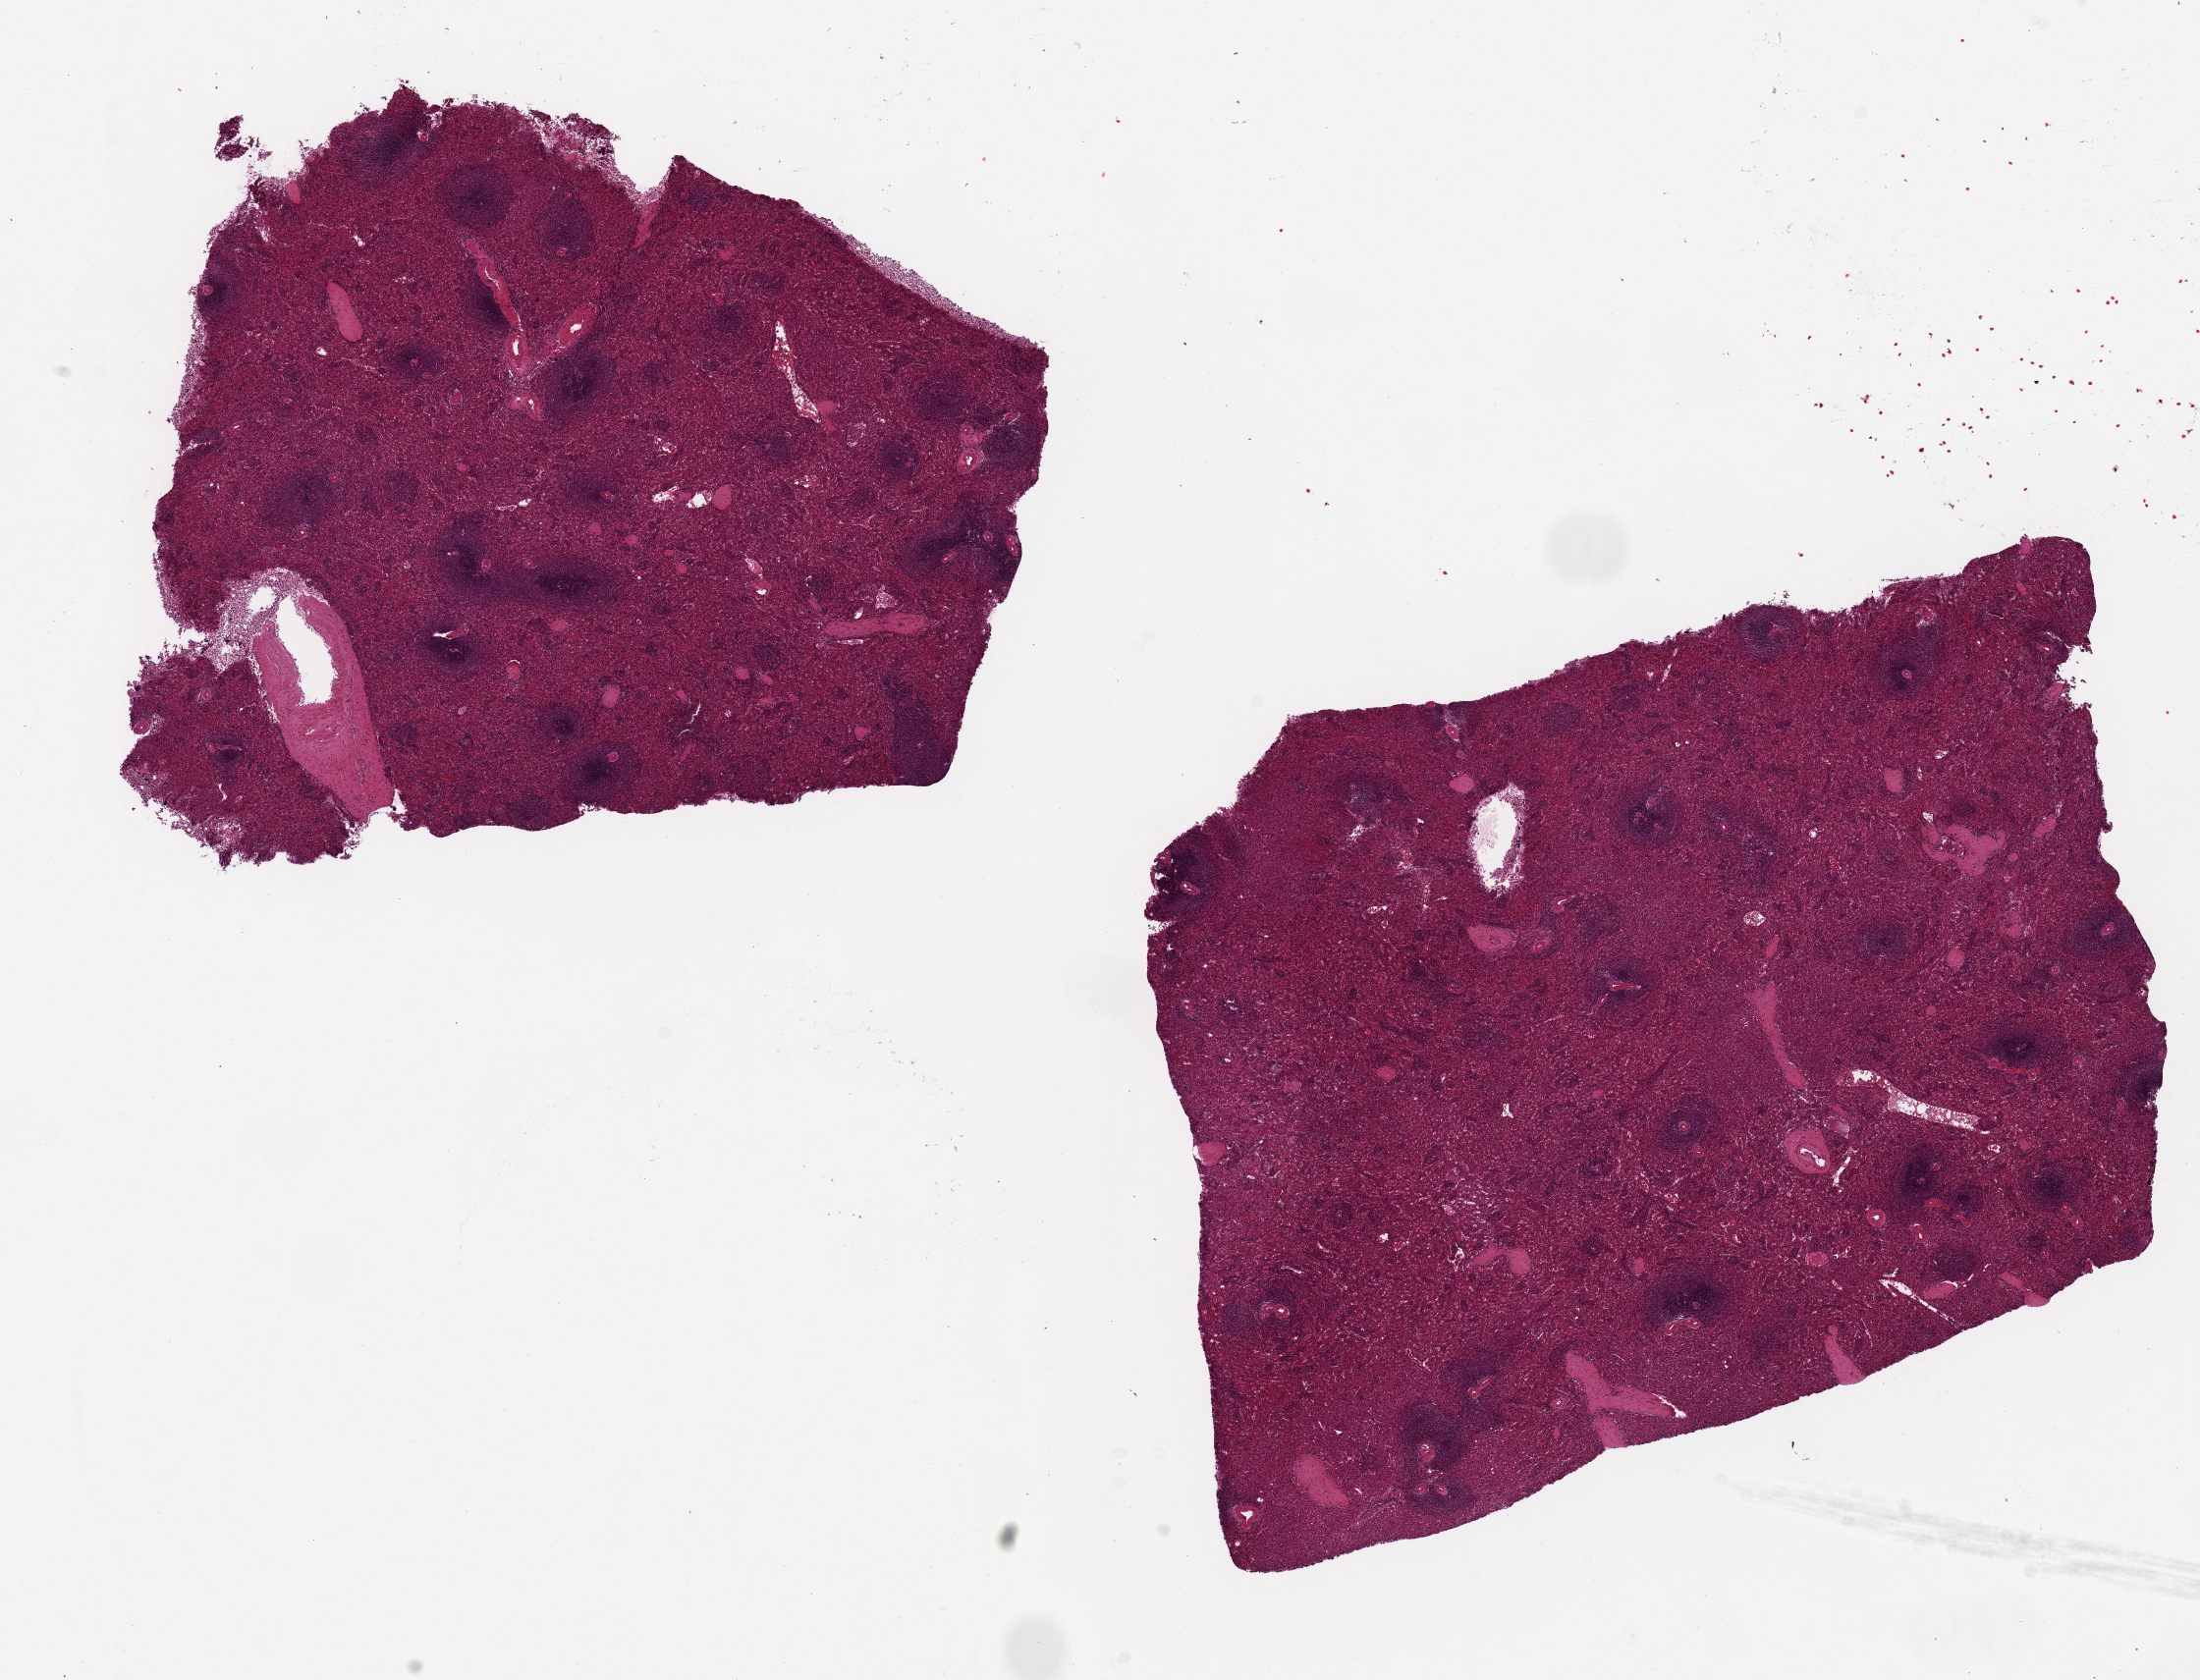
Haematoxylin and eosin whole-slide image — a low-resolution overview of the entire scanned area, about 17.7 x 13.5 mm (acquisition: 20x scan); PAXgene-fixed, paraffin-embedded tissue; sampled site (target tissue): spleen; tissue donor sample. Donor: male.
- pathologist's review note for this sample: 2 ~7.5x5.5mm aliquots